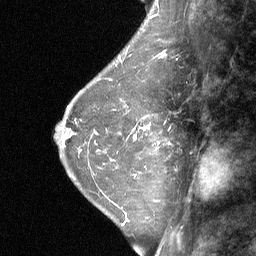
Breast MRI (dynamic contrast-enhanced), one sagittal slice; slice 20 of 64 in the series (ordered by position); dynamic contrast-enhanced study with each time point stored as its own series, time point 2 of 3 at this slice position (early post-contrast, ordered by acquisition time); 1.5 T; TE 4.8 ms, TR 27 ms; 2 mm slice thickness; 256 × 256 image matrix. Patient: female, 42 years. From the clinical record (not read from this slice): setting: breast cancer imaged before/during neoadjuvant chemotherapy; receptor status: triple-negative.
Annotated regions visible in this slice (semi-automatic segmentation, software-assisted and operator-edited):
- analysis volume of interest (the breast-tissue region the enhancement analysis was run in; not a lesion): bounding box [x1, y1, x2, y2] px = [124, 98, 176, 161]
- tumour enhancement mask (voxels above the 90 % enhancement threshold inside the analysis volume of interest): [133, 125, 149, 139]